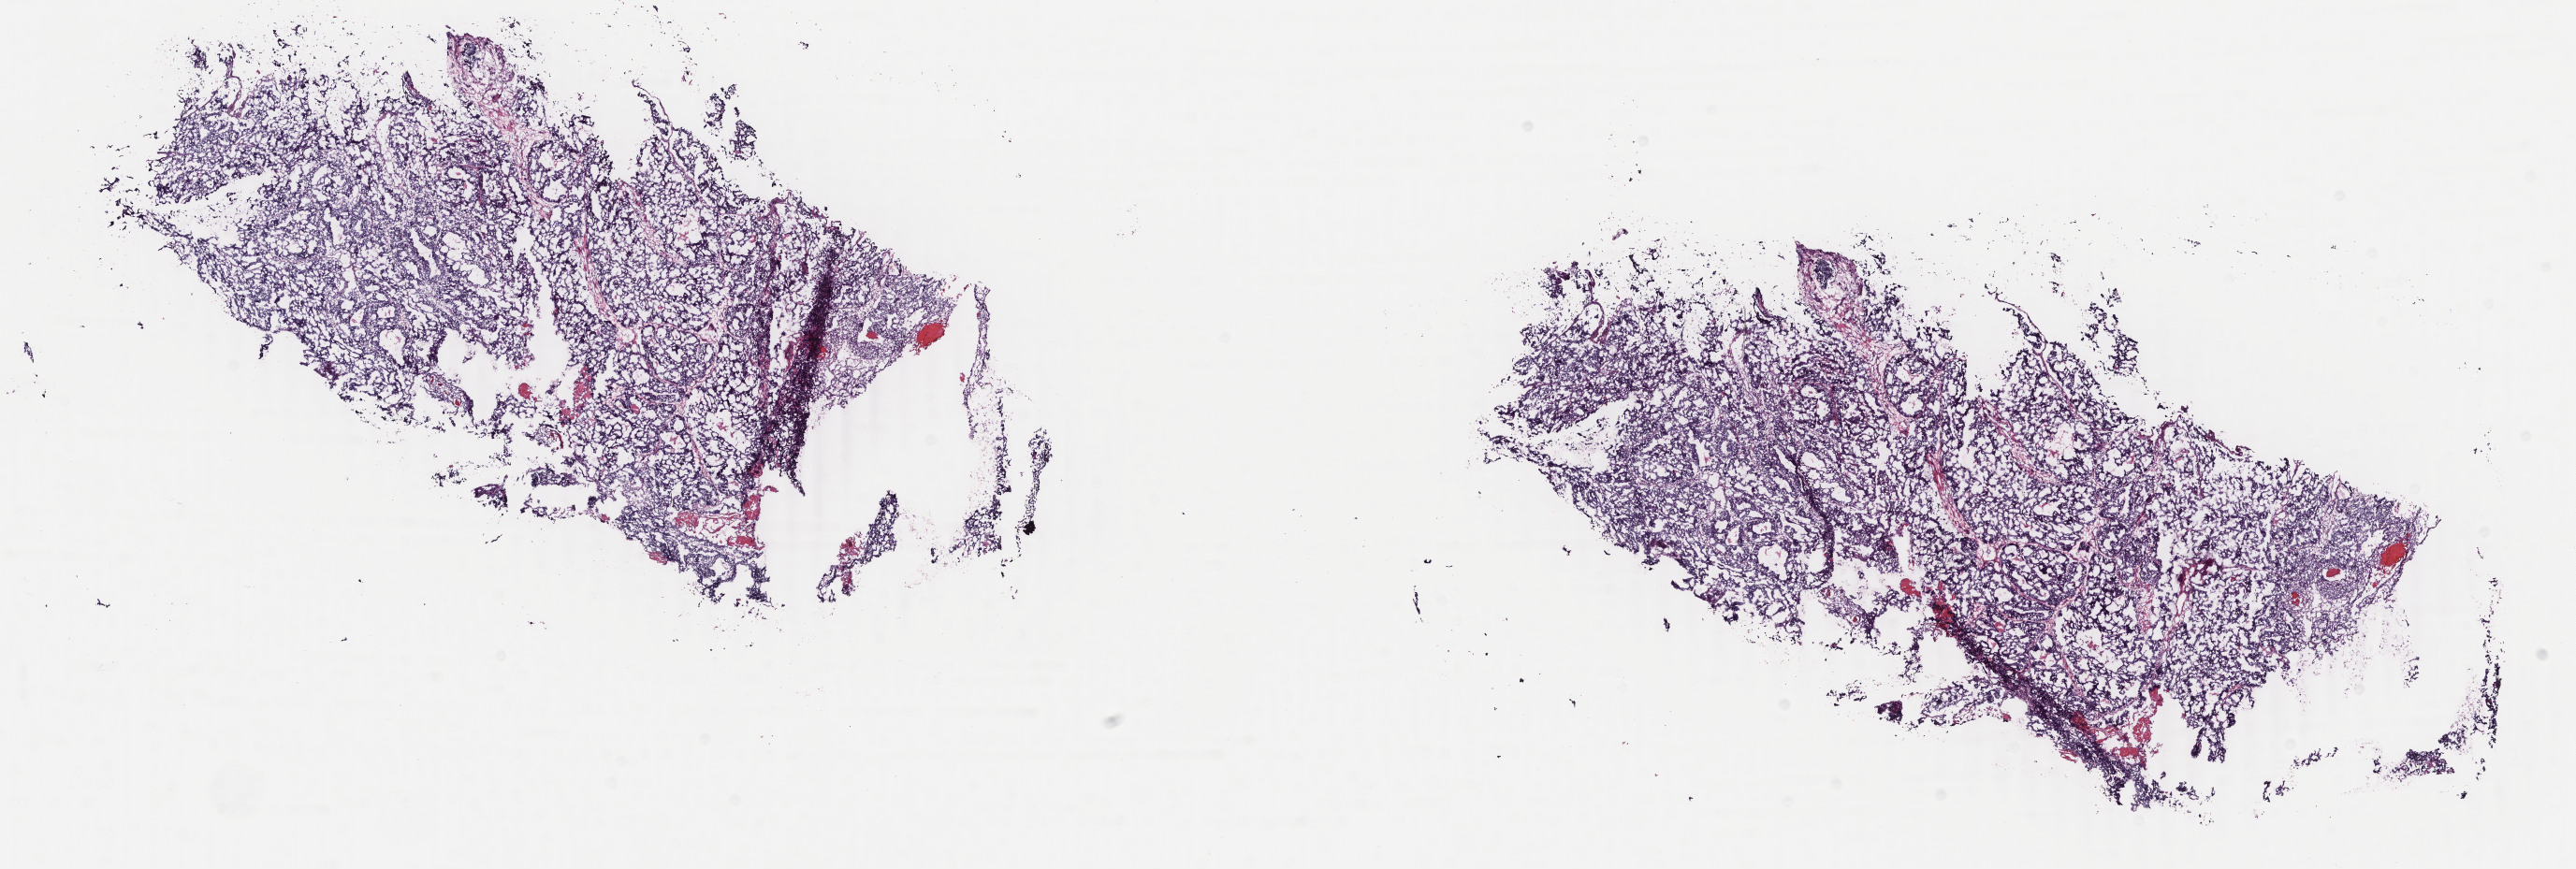
Whole-slide histology image, H&E-stained — a low-resolution overview of the entire scanned area, about 21.9 x 7.4 mm (slide scanned at 40x); frozen section; primary tumour sample from the uterus. Female, age 55 years at initial diagnosis.
Histologic diagnosis: Endometrioid adenocarcinoma, NOS (endometrium).